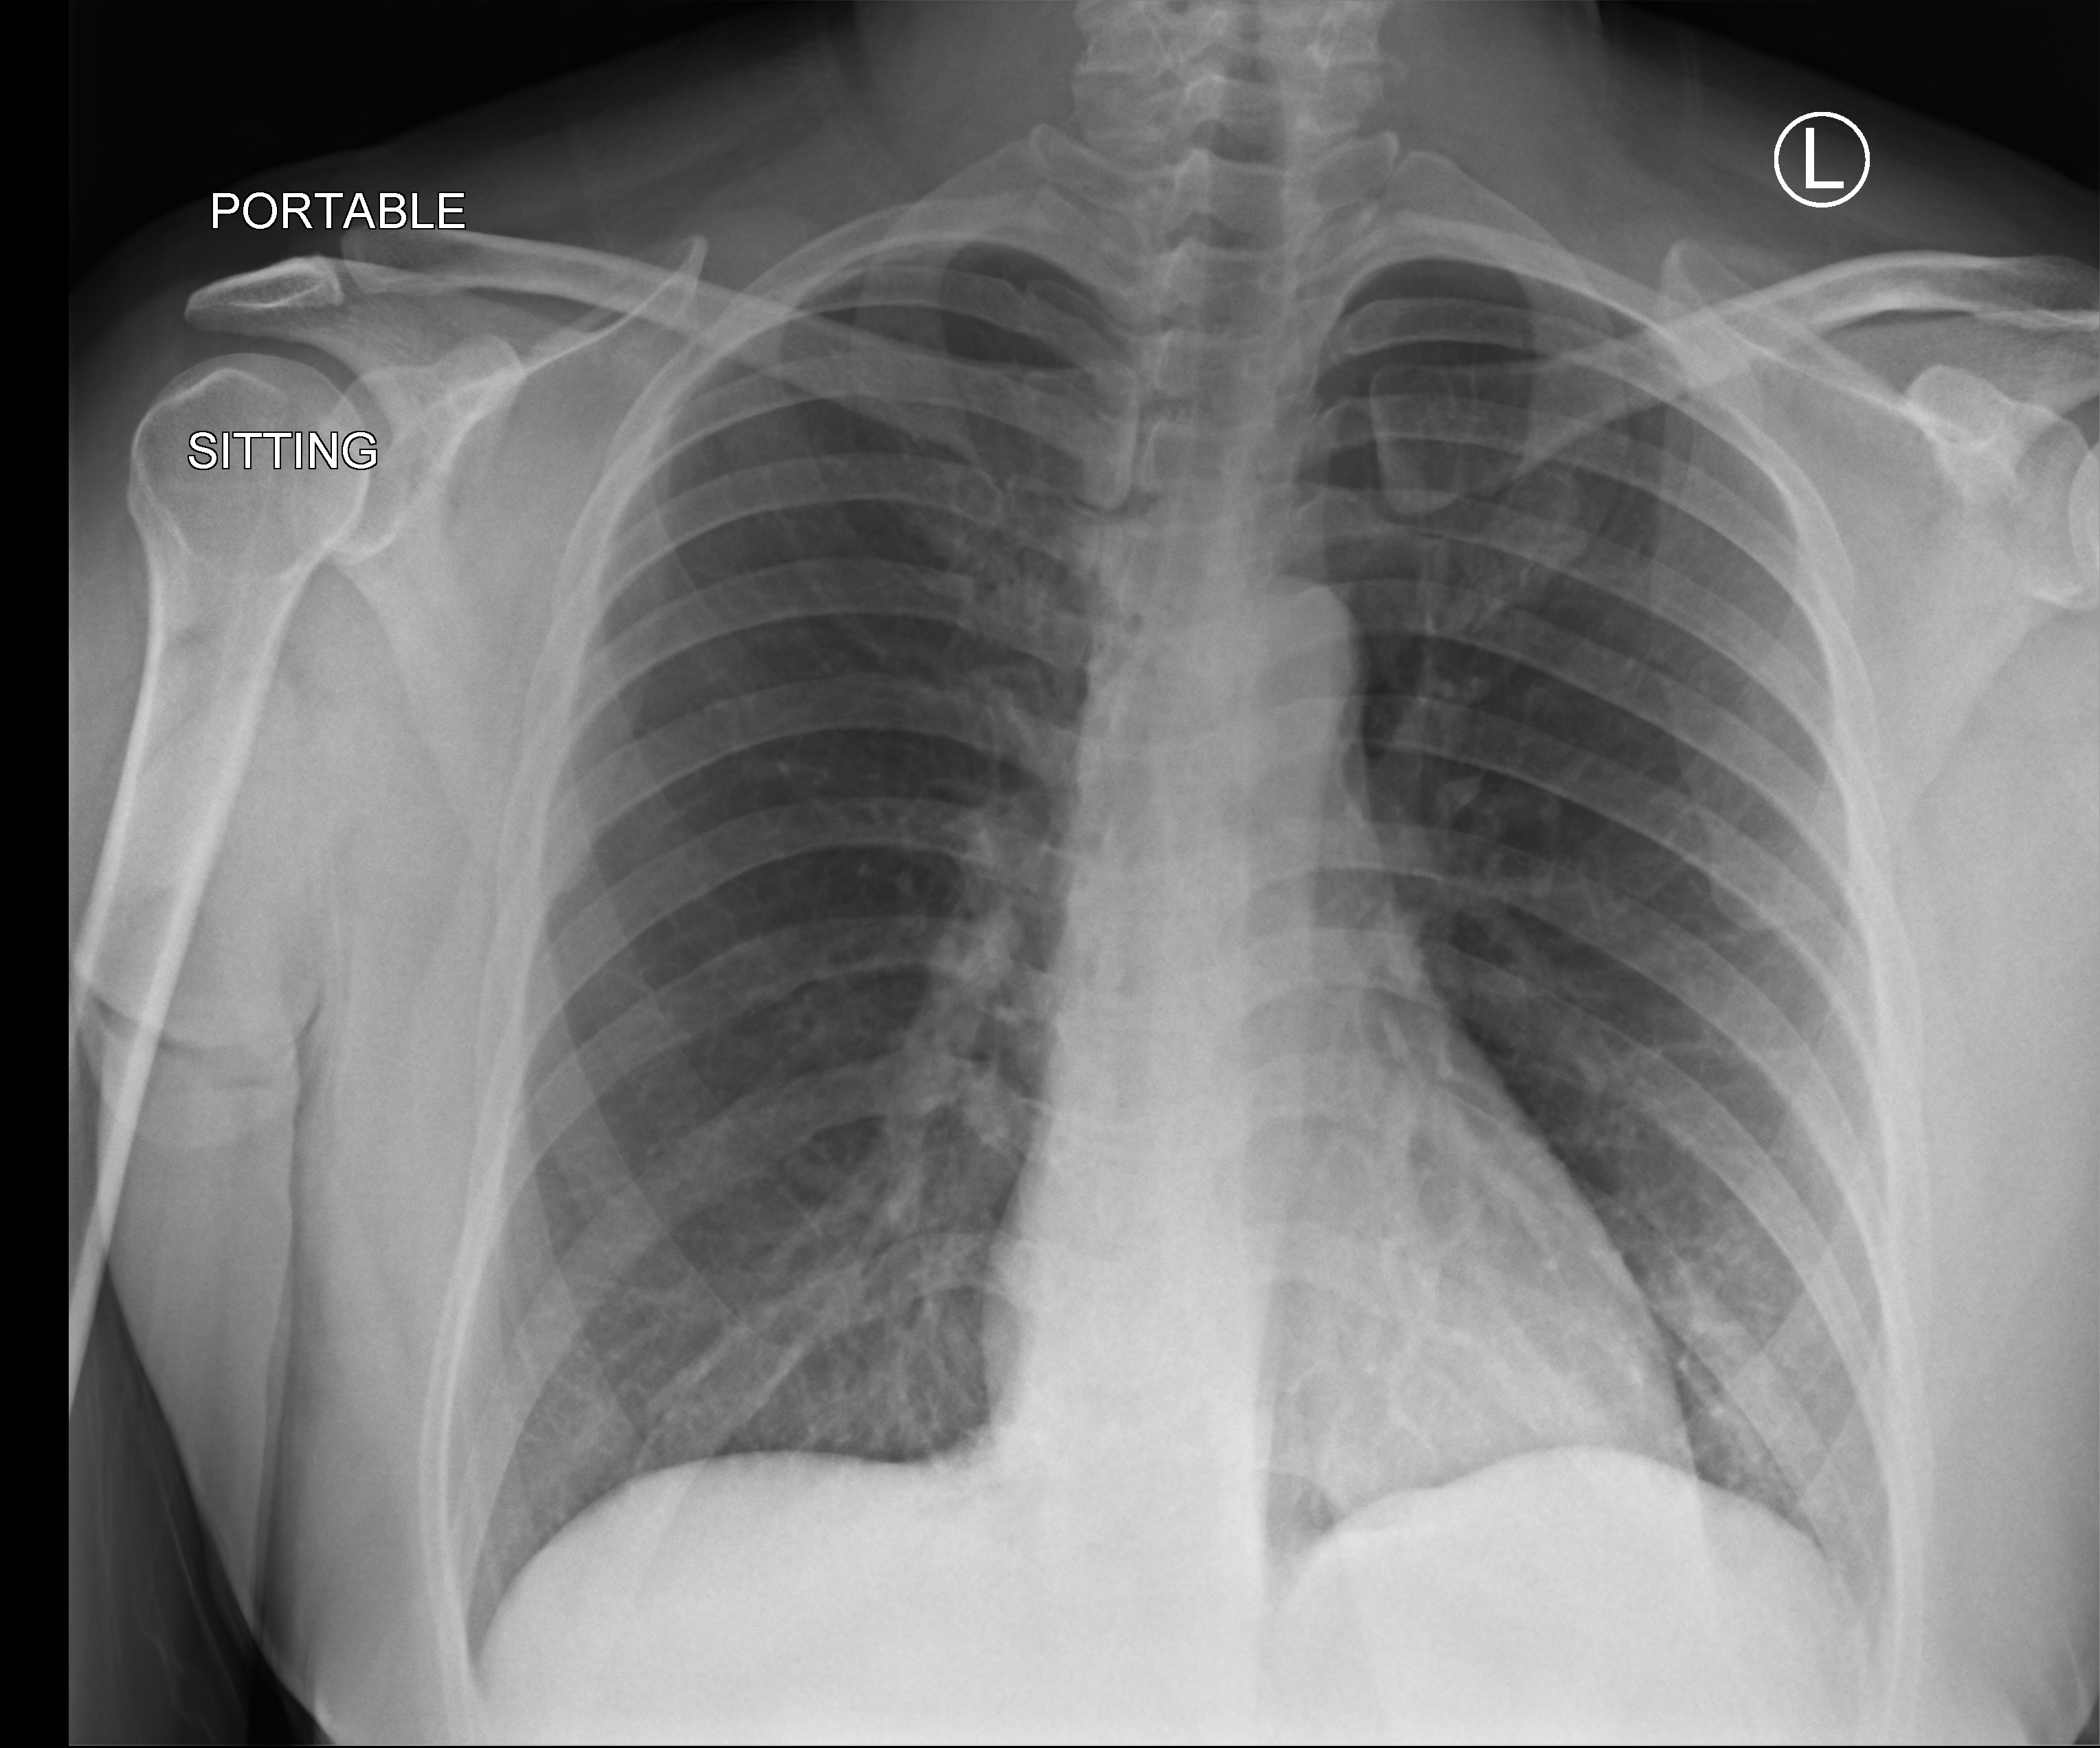
Portable chest radiograph; anteroposterior (AP) projection. Female patient hospitalised with COVID-19, age 18–59 years.
Hospital-stay facts (about this admission, not read from this image; timing relative to this image not recorded):
- admitted to intensive care during this hospital stay: no
- mechanically ventilated during this hospital stay: no